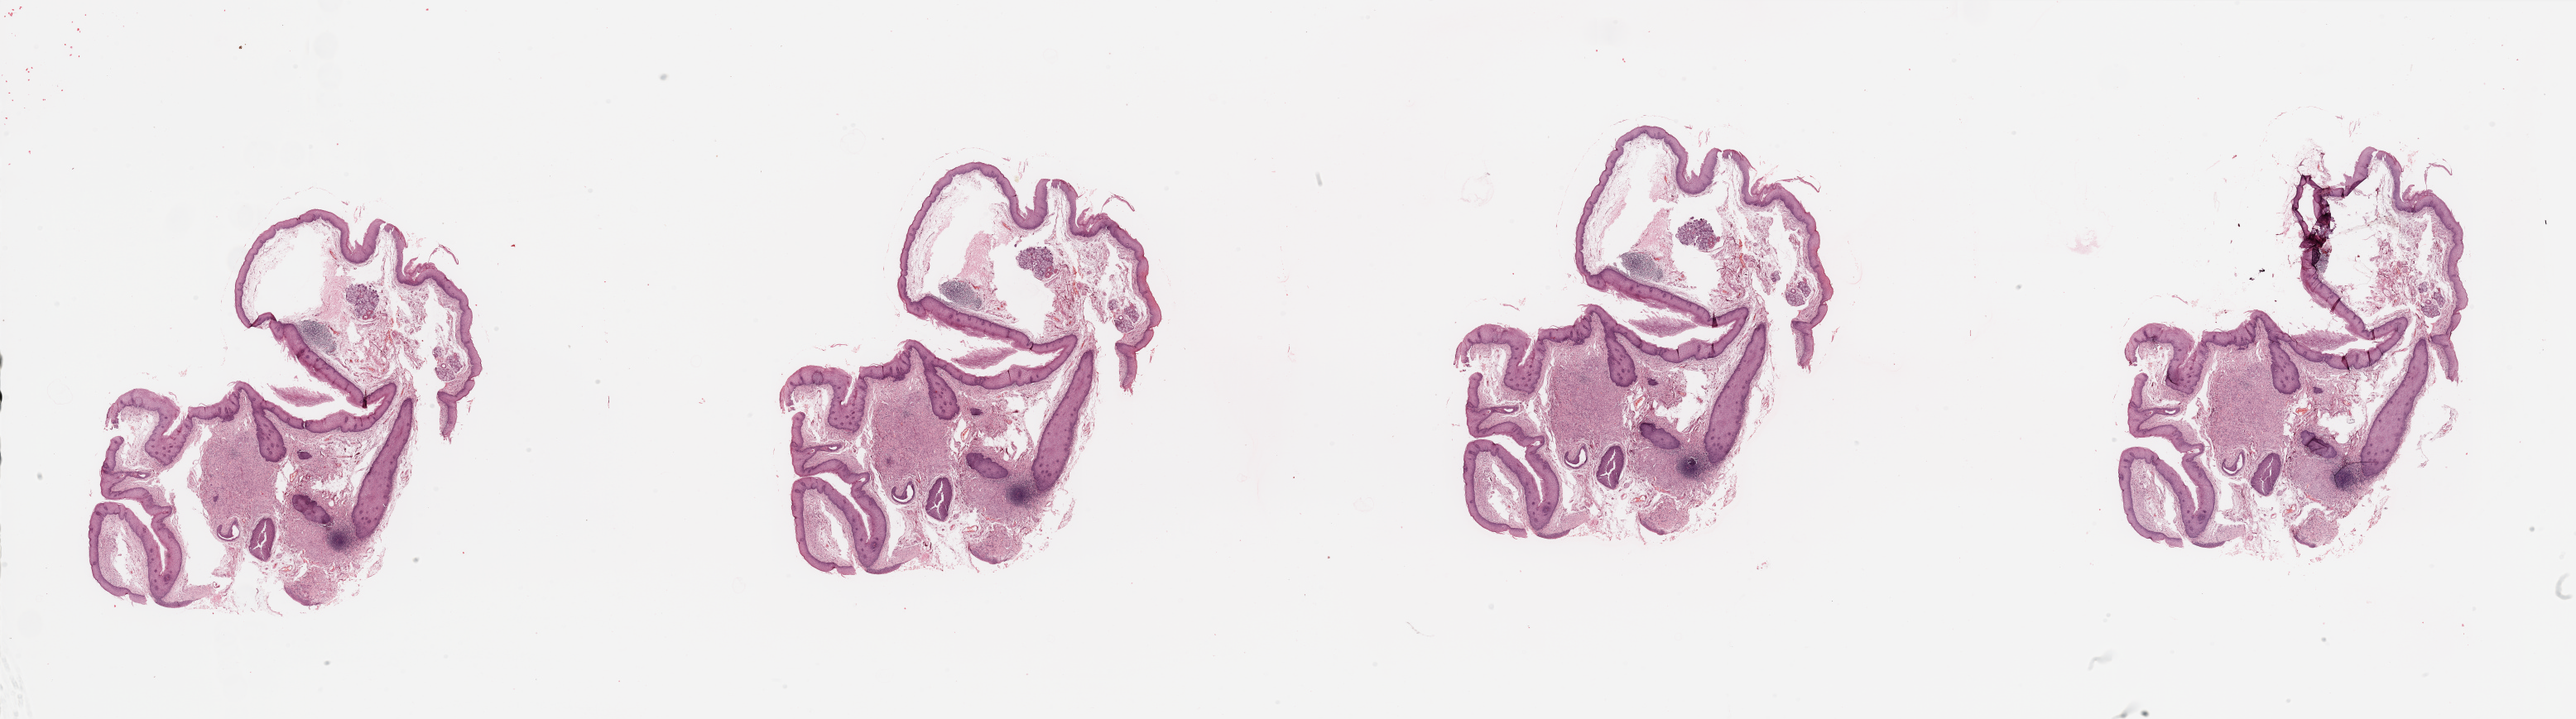
Whole-slide histology image, Hematoxylin and eosin (H&E) stained — low-resolution overview of the scanned area, about 49.2 x 13.7 mm. Normal (non-tumour) tissue sample, sampled site: larynx. Male, 81 y/o.
This section: normal (non-tumour) tissue from the same patient. Patient diagnosis: Squamous cell carcinoma, NOS (larynx, NOS).